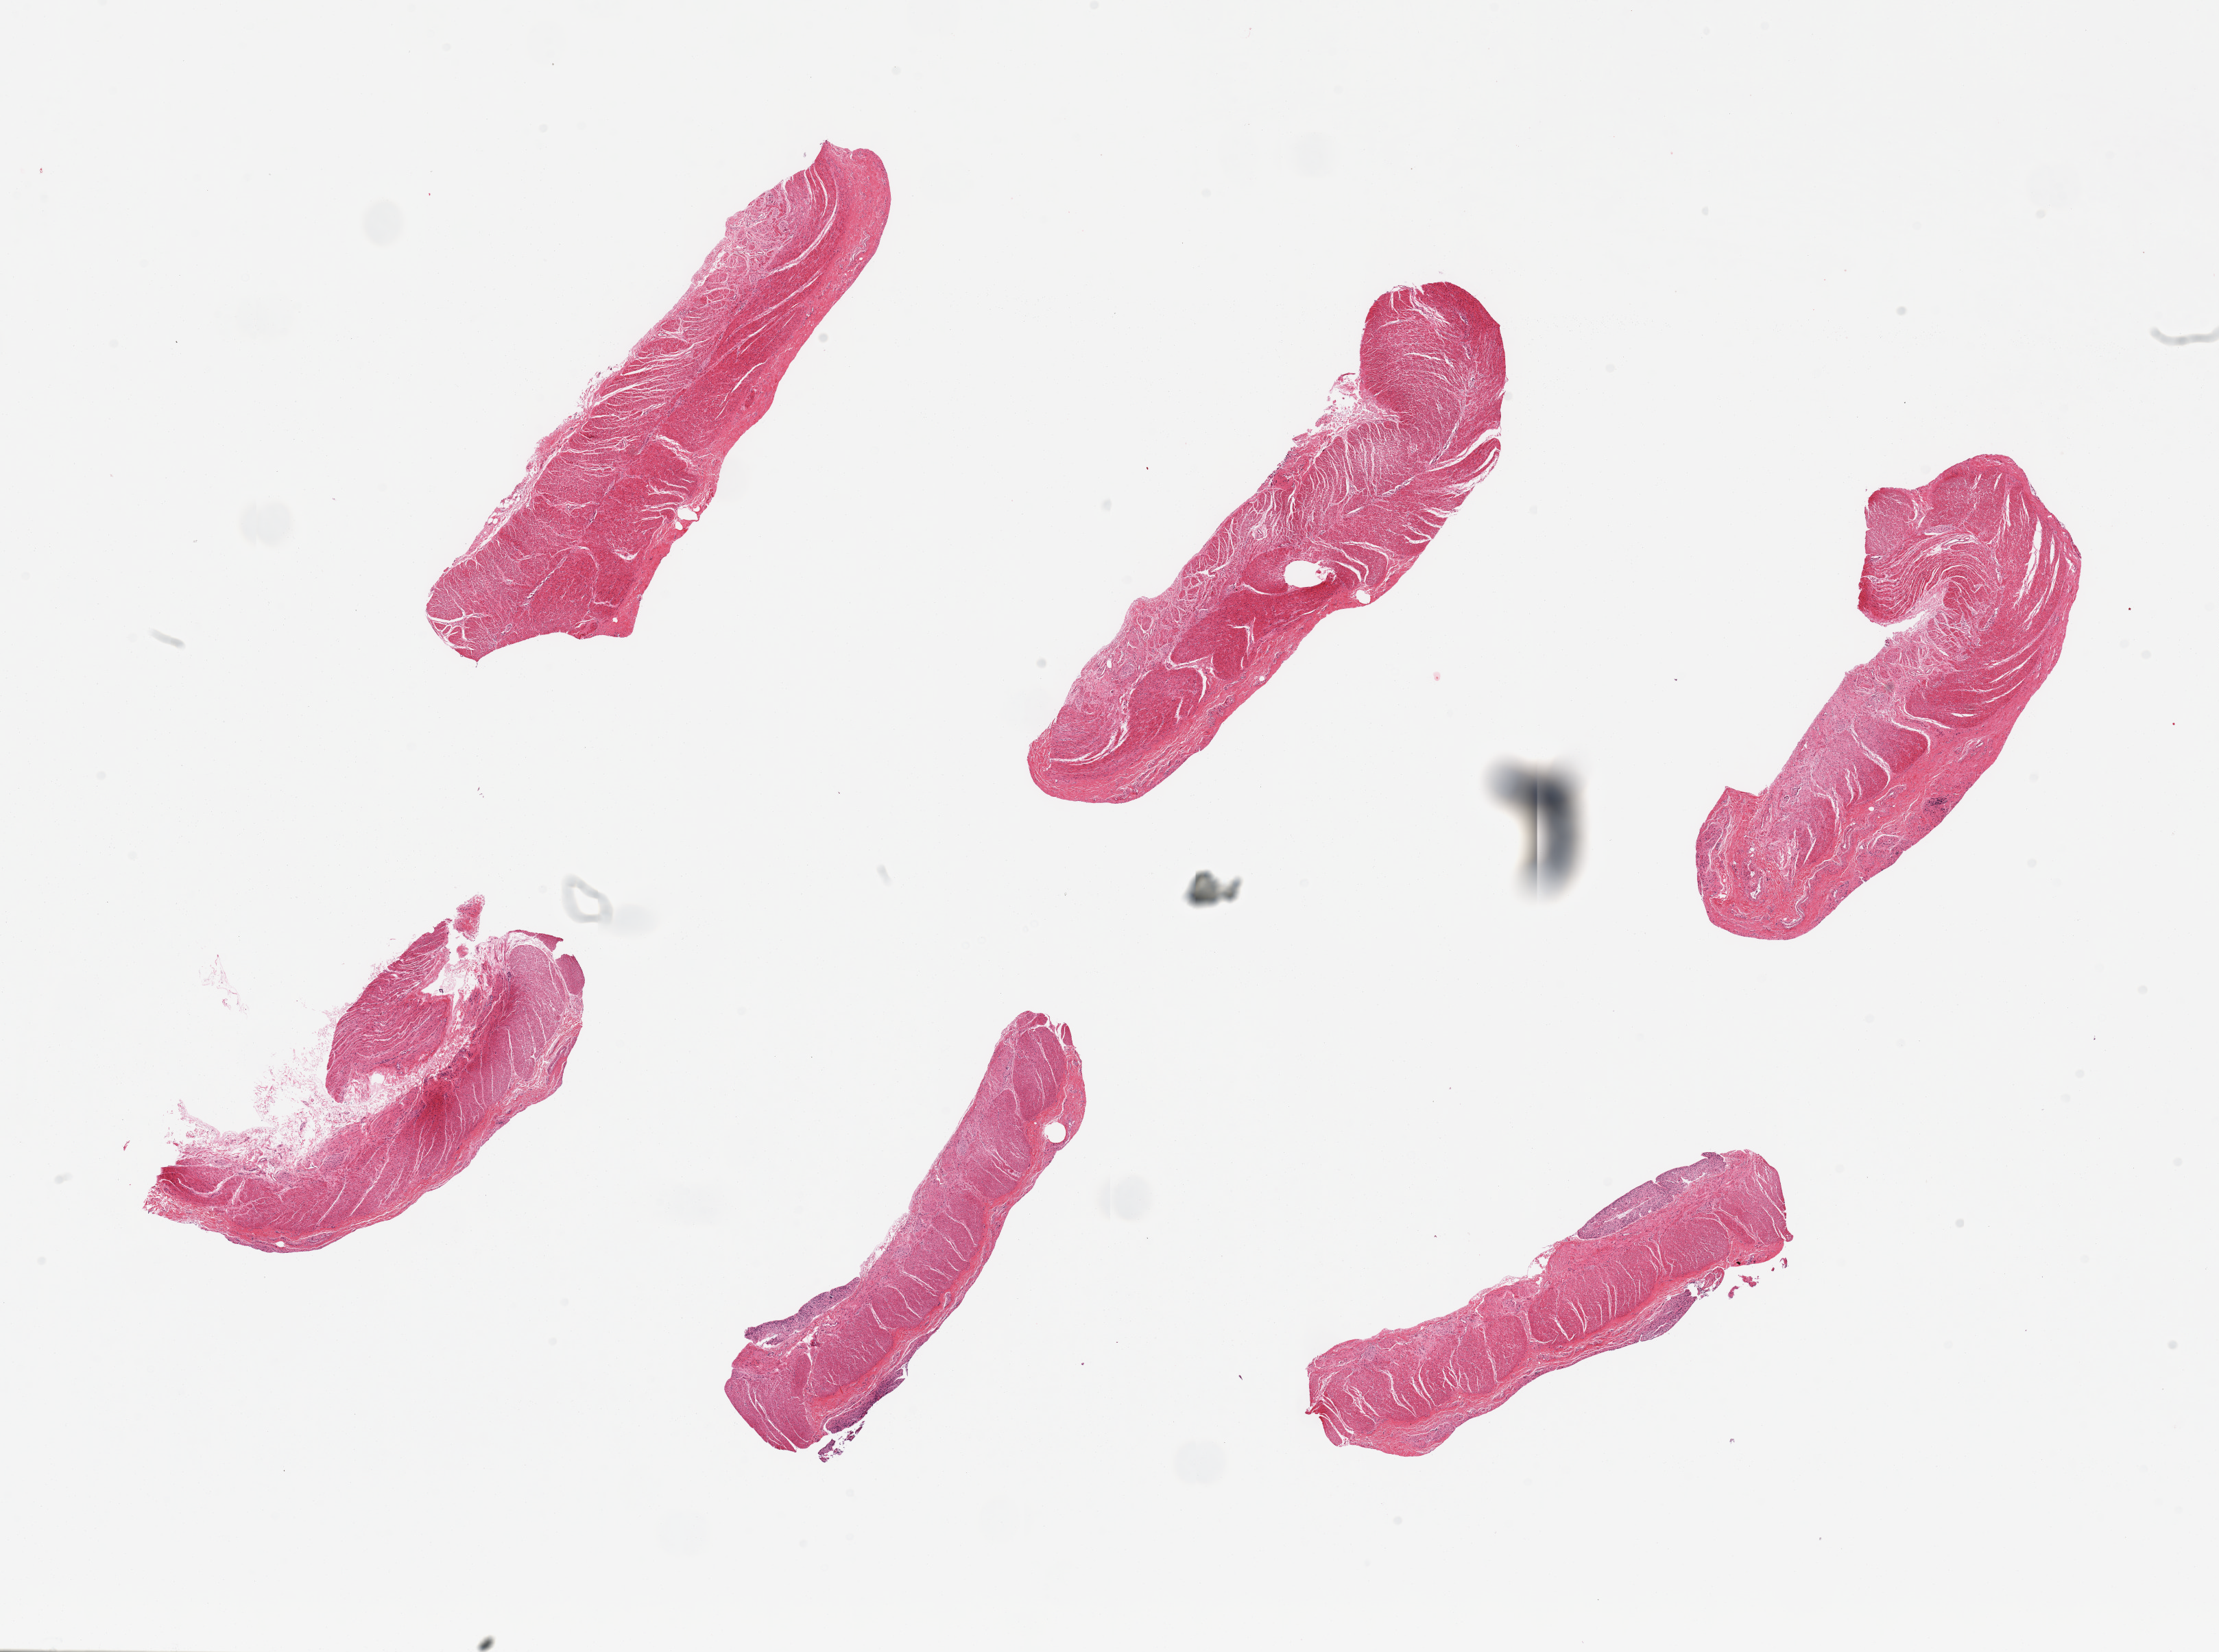
Digitized hematoxylin and eosin (H&E)-stained section, low-resolution overview of the scanned area, about 25.6 x 19.1 mm (acquisition: 20x scan); PAXgene-fixed paraffin-embedded (PFPE) section; sampled site (target tissue): sigmoid colon; donor tissue sample. Donor: female.
• review note (as recorded): 6 pieces; all muscle; well trimmed